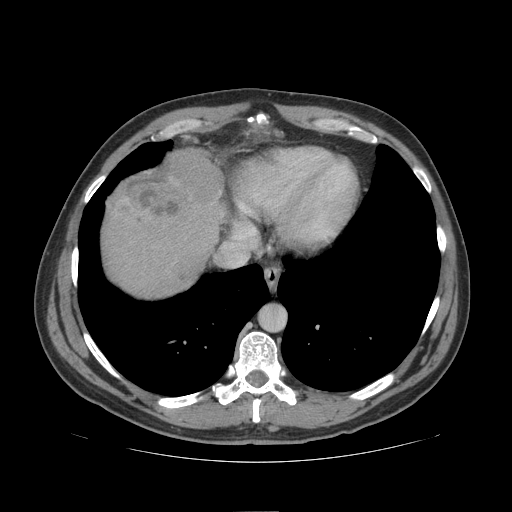
Contrast-enhanced abdominal CT (liver protocol), one axial slice. Position 92 of 109 along the scan axis. 140 kVp. Soft-tissue window (W 400 / L 40 HU). 512 × 512 image matrix, field of view 420 × 420 mm. Case-level facts recorded for this patient, not image findings: diagnosis: hepatocellular carcinoma (patient treated with transarterial chemoembolisation; whether this scan precedes or follows treatment is not stated here); TNM stage (as recorded): Stage-IIIB.
Annotated regions visible in this slice (semi-automatically segmented with operator editing):
- liver parenchyma outside the tumour (the mass and vessels are separate outlines, so this box may not span the whole liver): box from (x=102, y=158) to (x=228, y=296) px
- mass: (x=115, y=147)–(x=222, y=224)